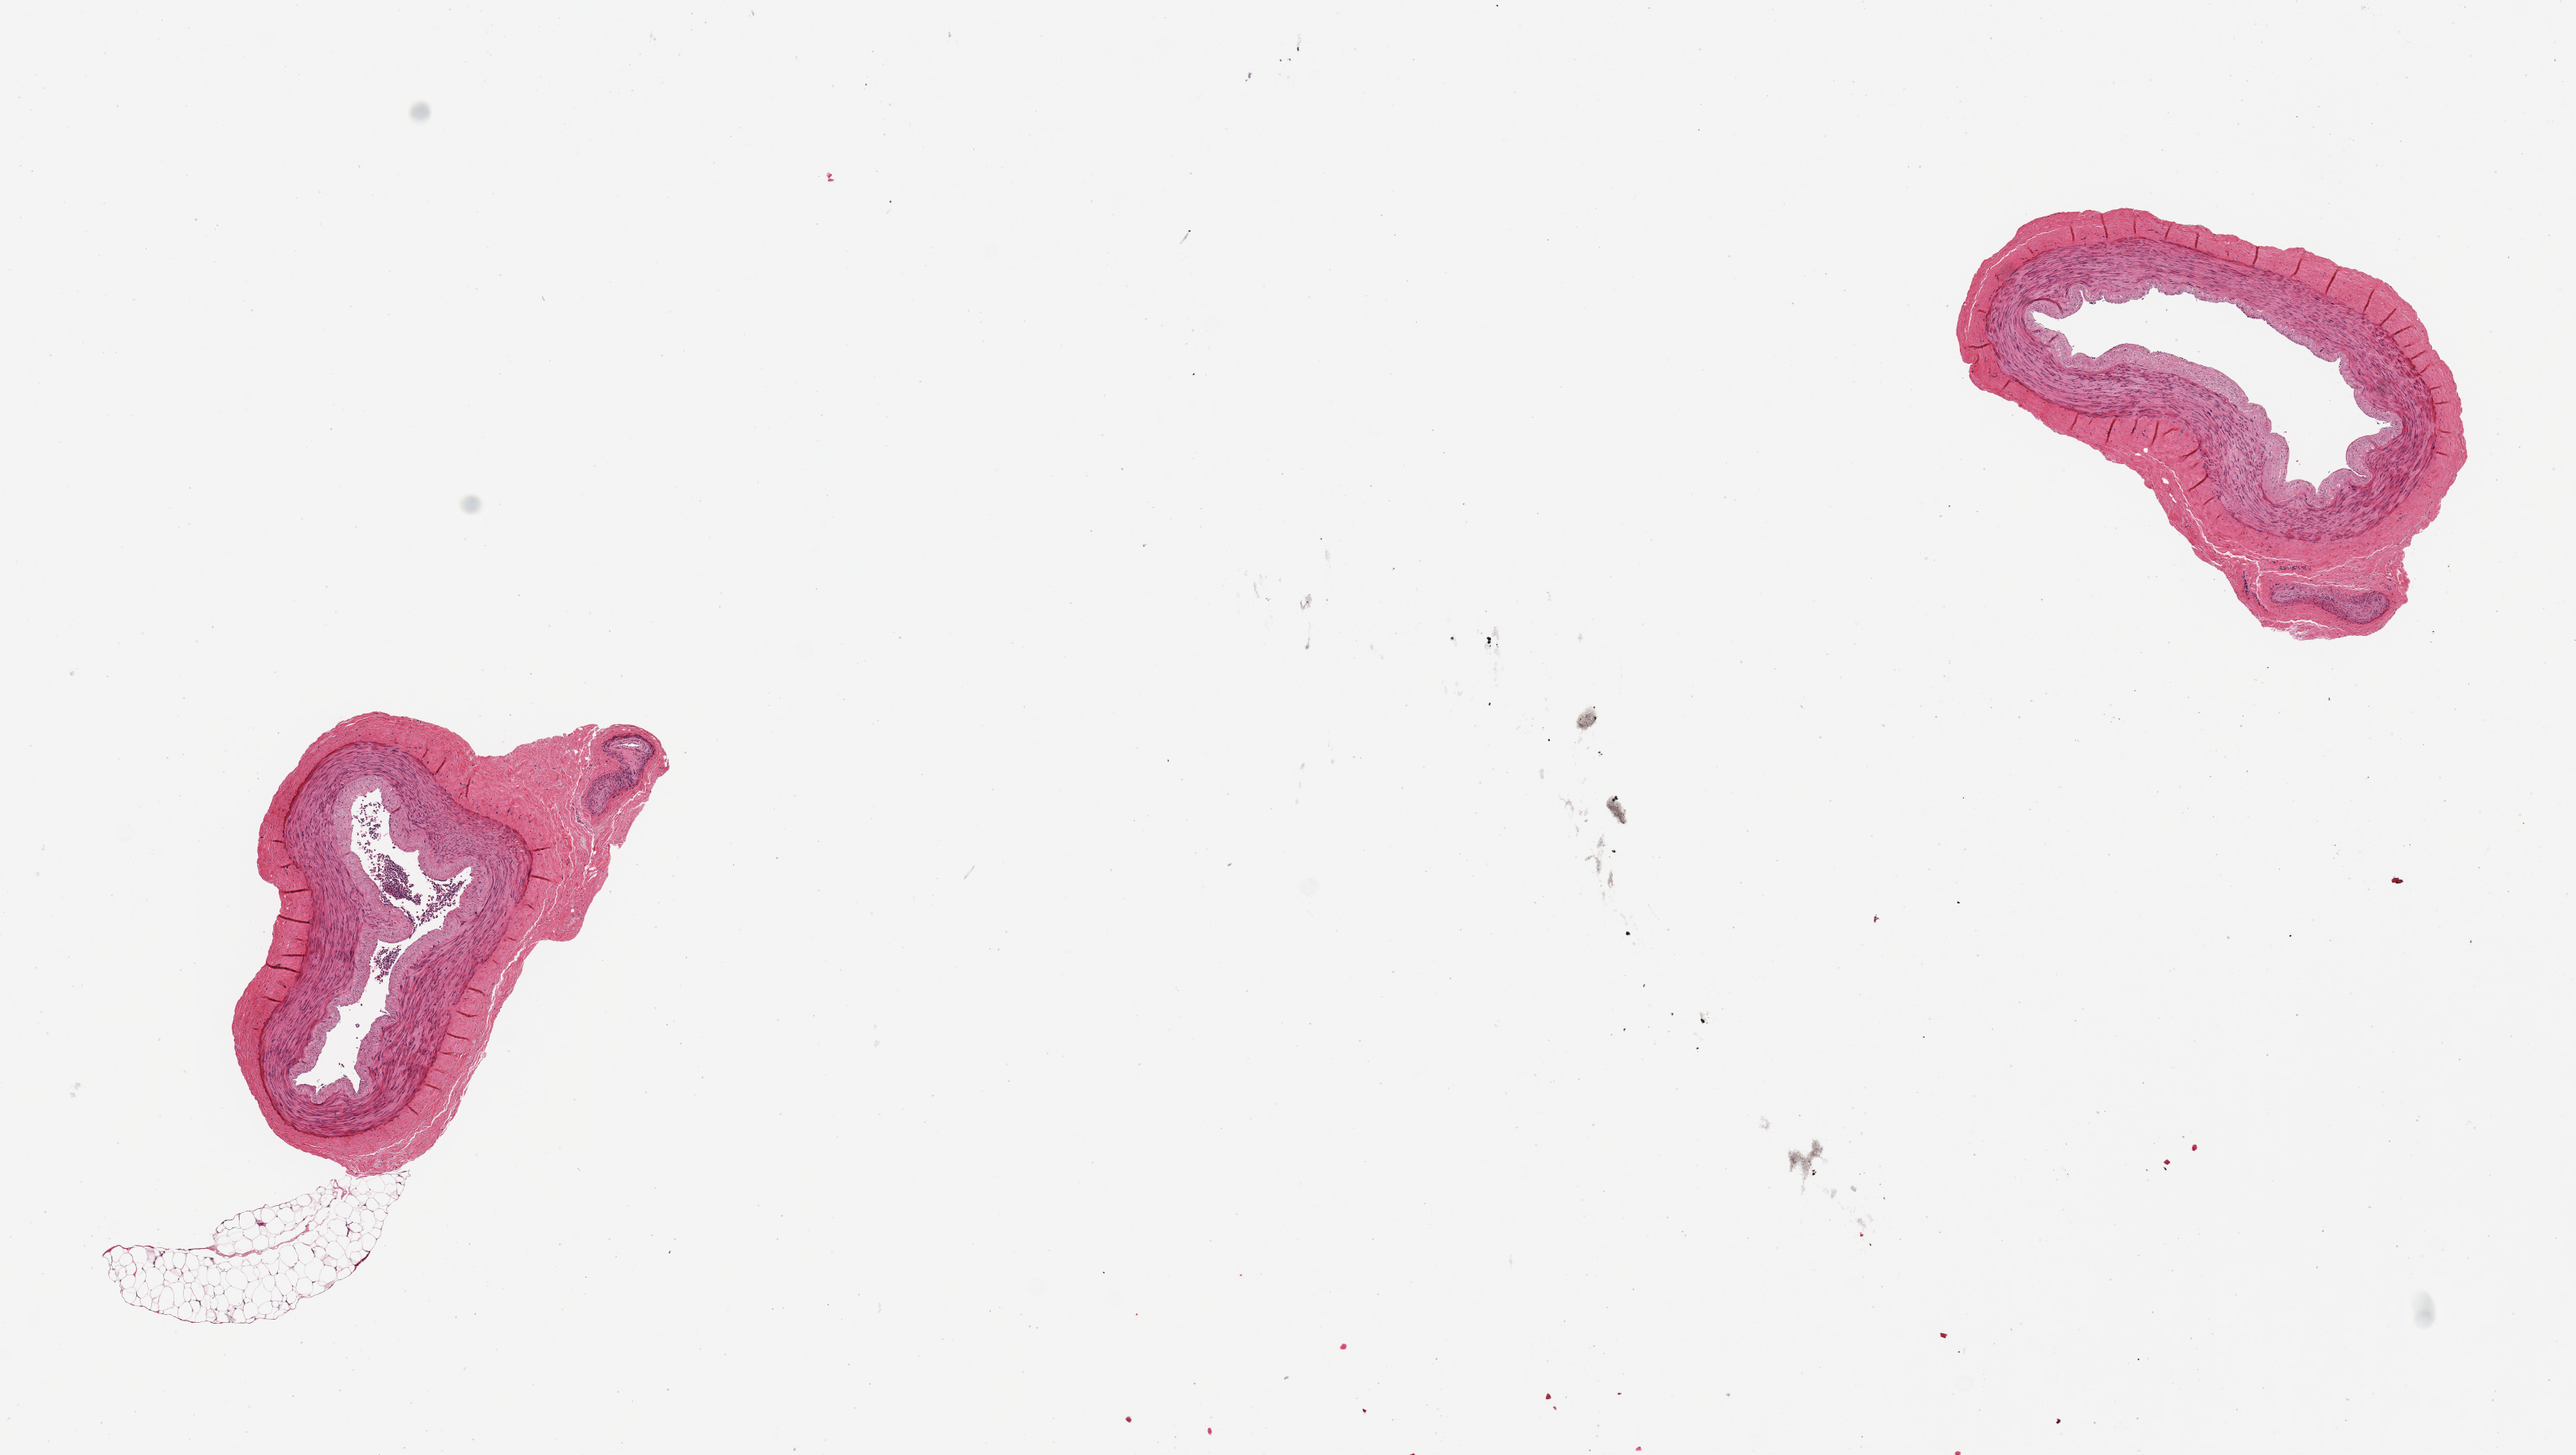
Haematoxylin and eosin whole-slide image — shown as a low-resolution overview of the whole scanned area (about 12.8 x 7.2 mm). PAXgene-fixed paraffin-embedded (PFPE) section. Target tissue: tibial artery. Donor tissue sample. Donor: male.
Reviewer comment on this tissue sample: 2 pieces, no atherosis, clean specimen without adherent fat.